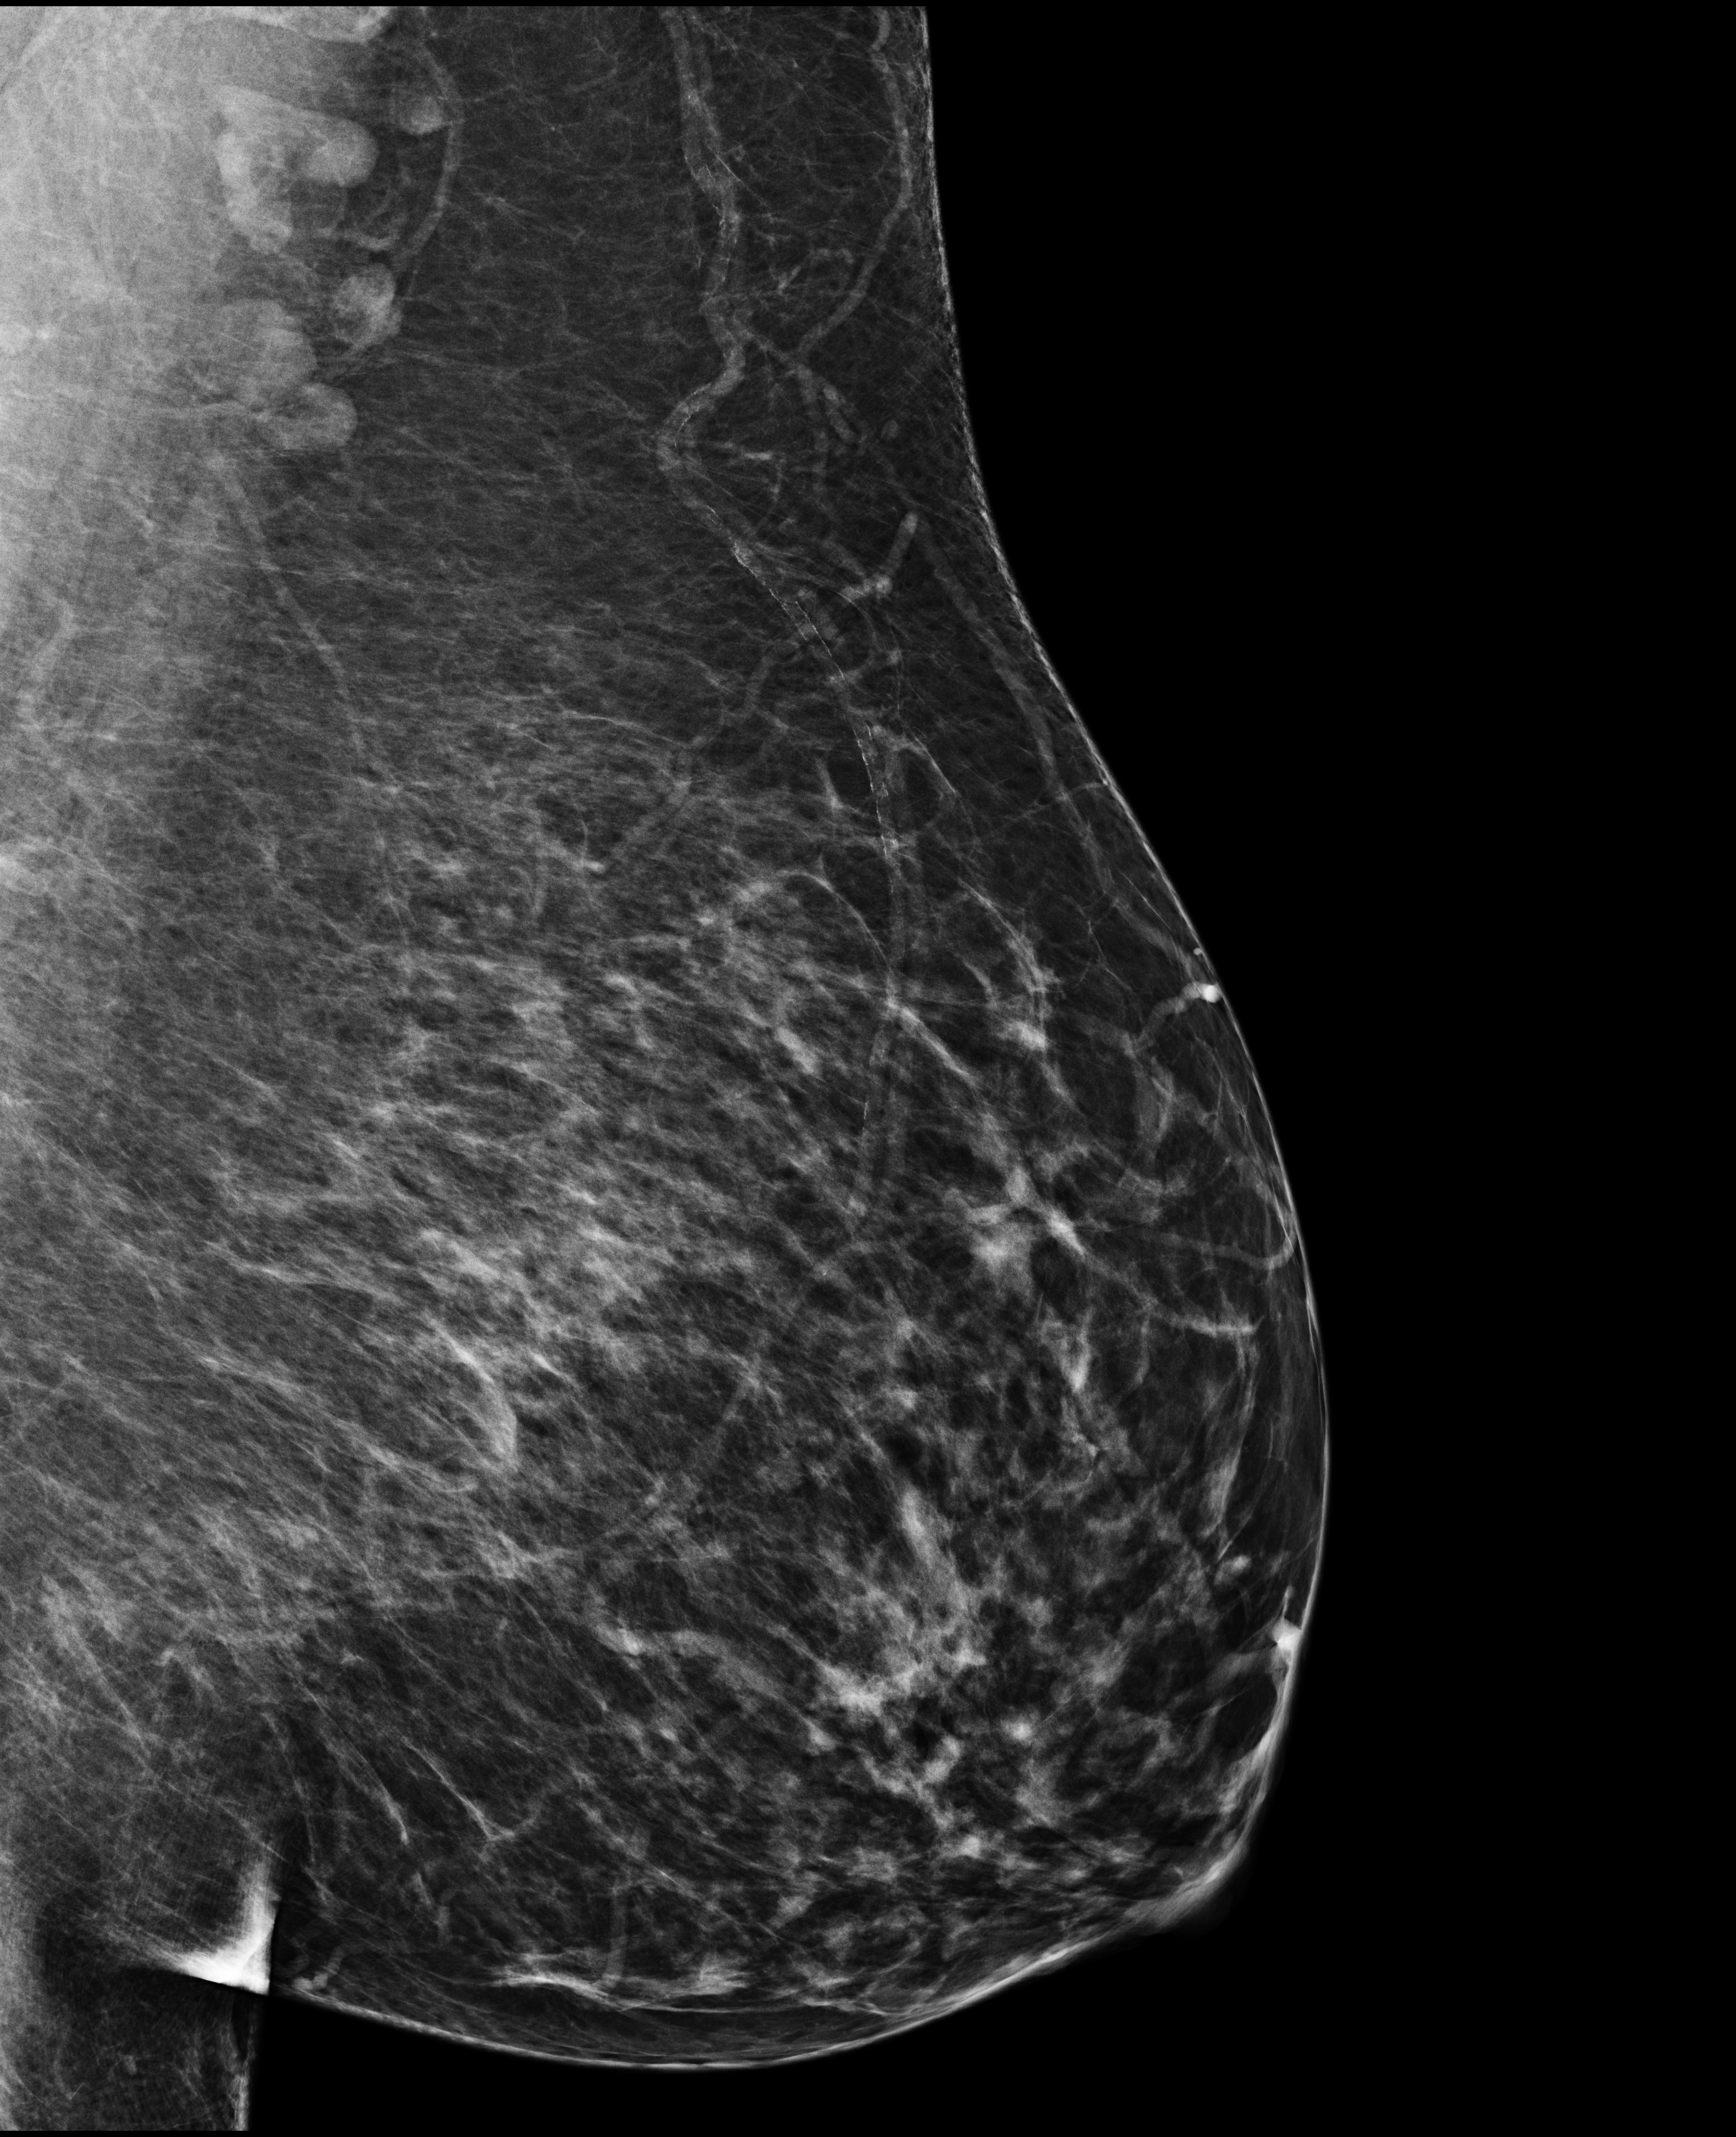
Digital mammogram (FFDM), left breast, MLO view, annual screening mammography examination, compressed breast thickness 87 mm, system: Selenia Dimensions. Patient aged 67 years (female).
BI-RADS breast density category at the screening exam (both breasts, scale 1–4): 2. Final BI-RADS category for the screening round (tomosynthesis exam, both breasts): category 1. Recall: no recall after this screen.